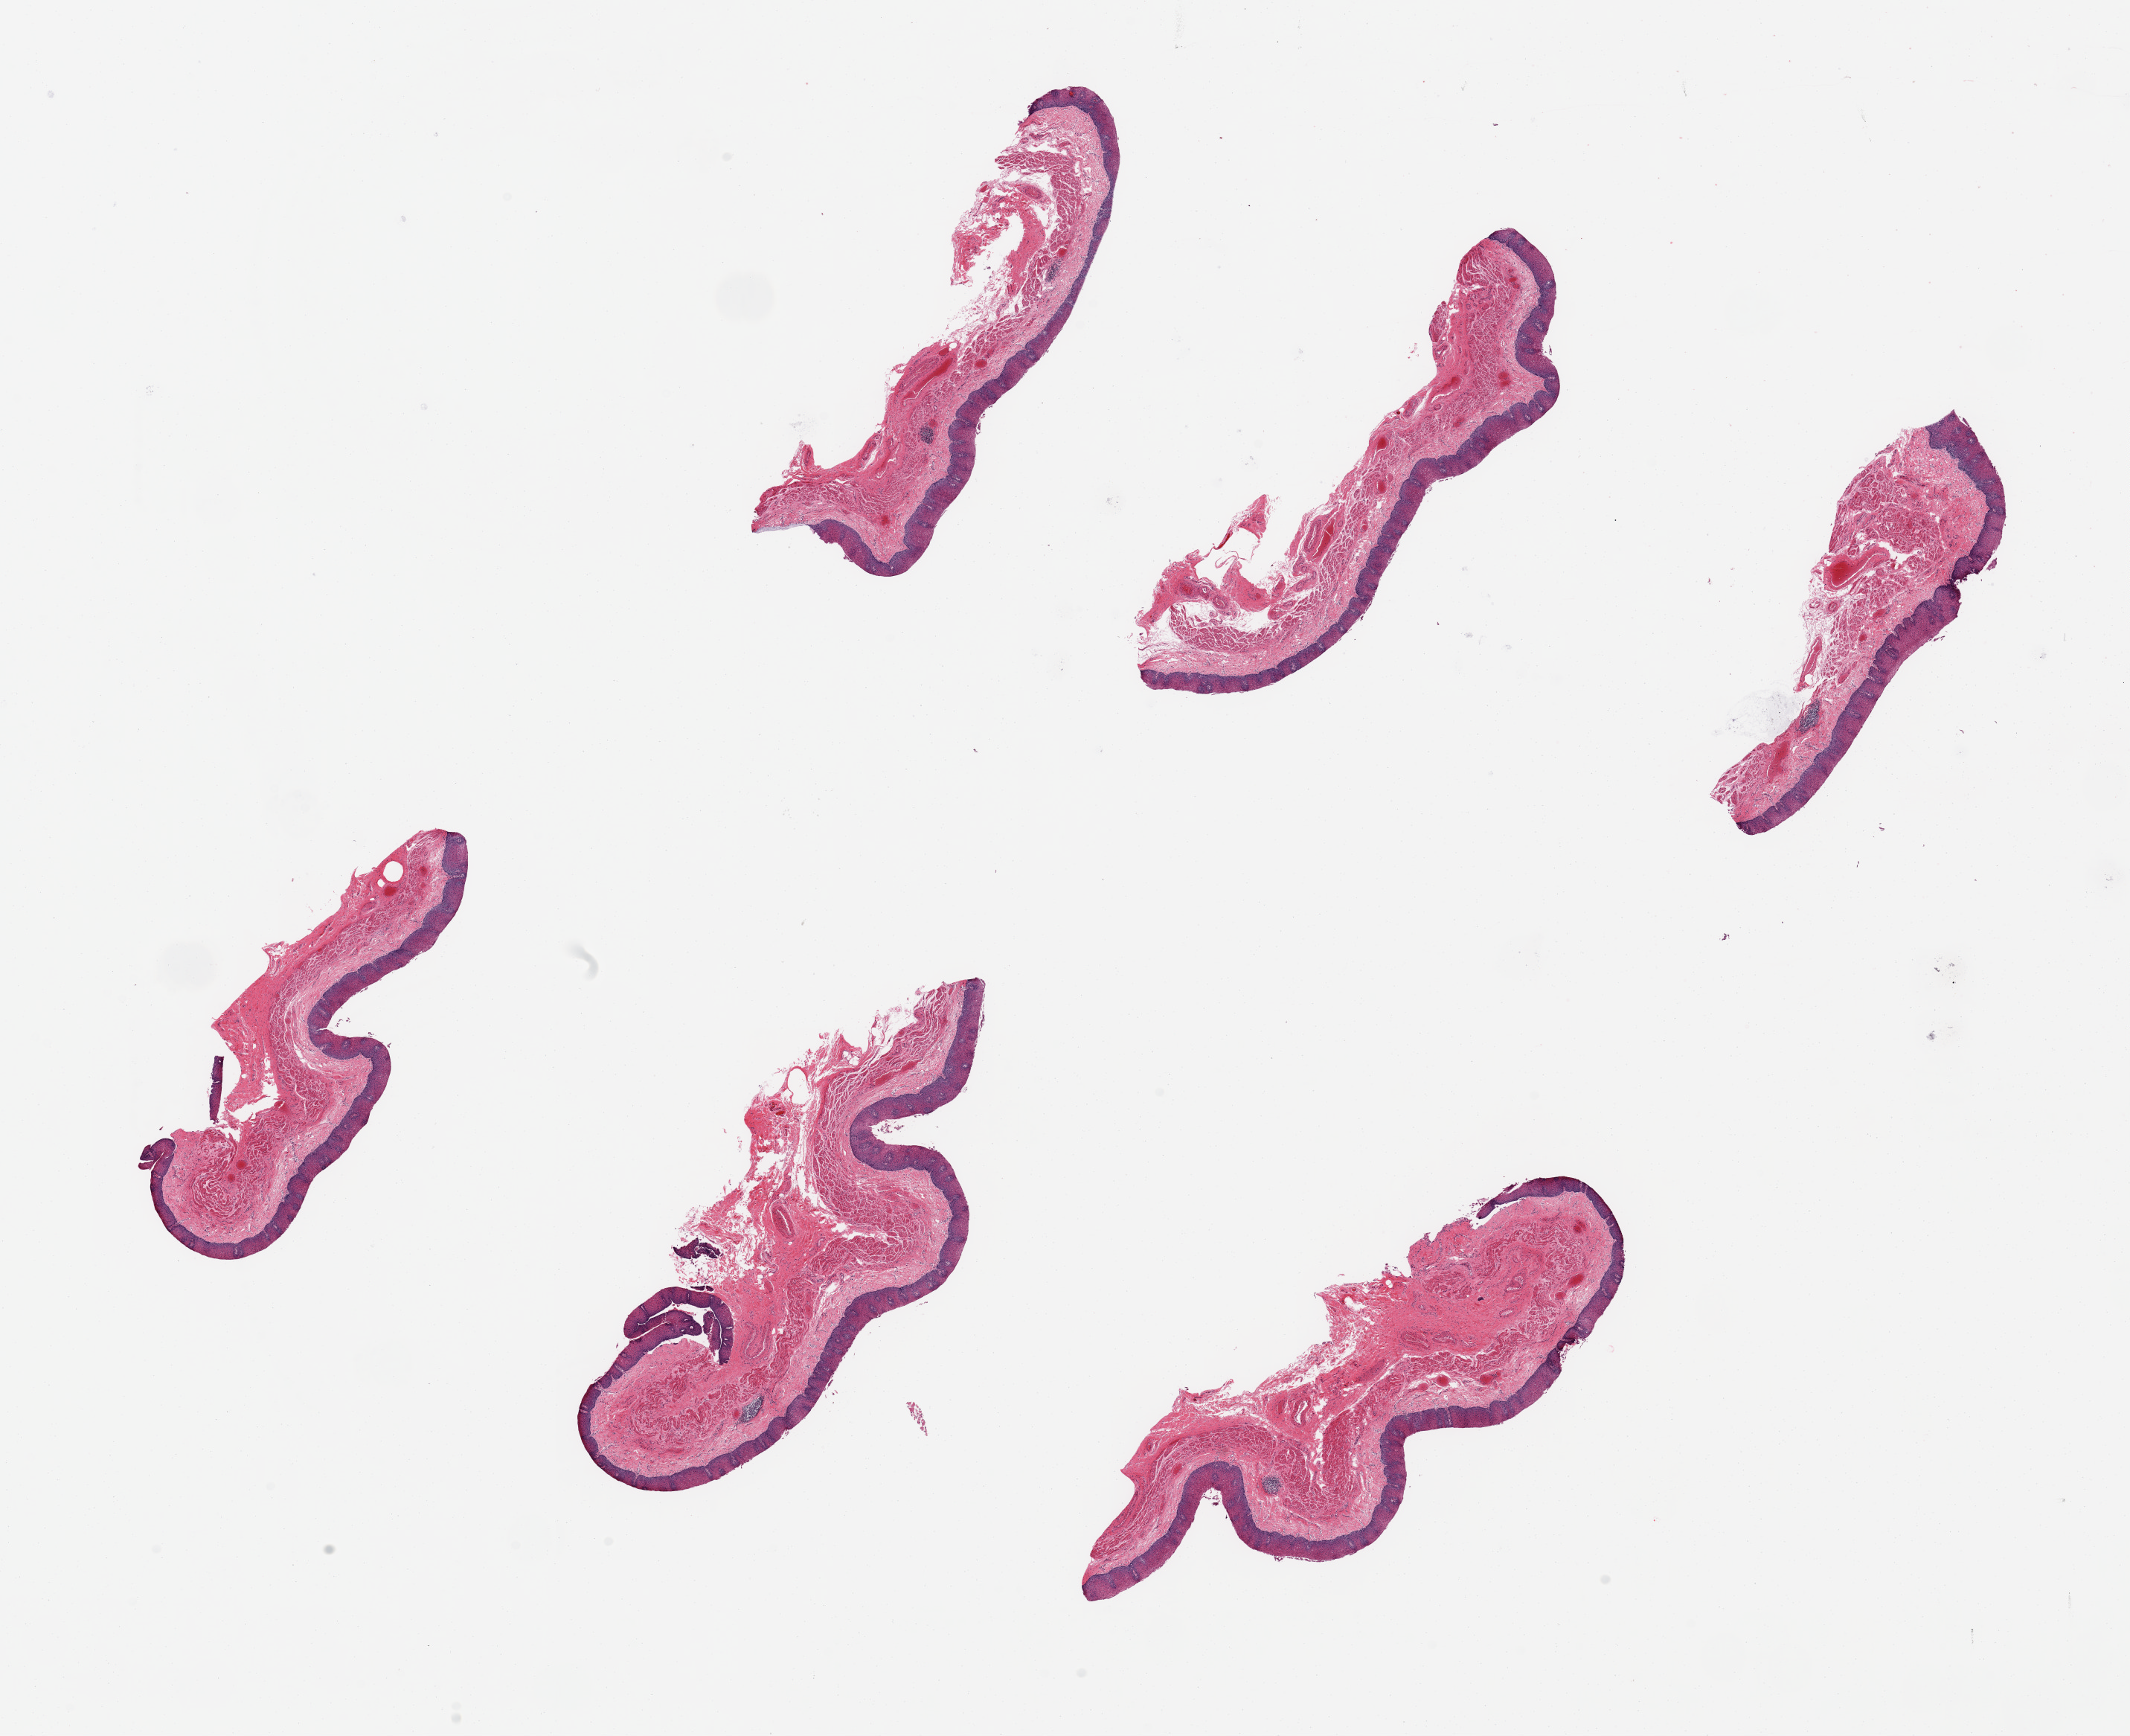
Digitized haematoxylin and eosin-stained section, brightfield — low-resolution overview of the scanned area, about 22.6 x 18.5 mm (from a 20x scan). PAXgene-fixed paraffin-embedded (PFPE) section. Sampled site (target tissue): esophageal mucous membrane. Donor tissue sample. Donor: male.
Pathologist's review note for this sample: 6 pieces,~6x1.2mm; epithelium 0.3mm.